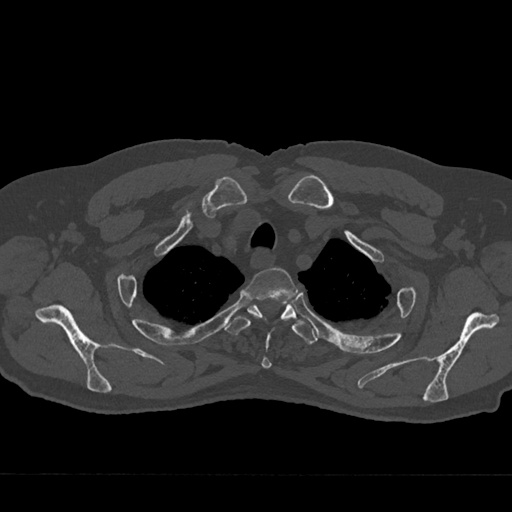
CT including the spine, one axial slice; slice 589 of 797 in the series (ordered by position); reconstruction kernel Br40s/3; 120 kVp; bone window (W 1800 / L 400 HU); 0.5 mm slice thickness; 512 × 512 image matrix, field of view 377 × 377 mm. Male patient, age 75 years. Case-level facts recorded for this patient, not image findings: primary cancer: renal; vertebrae with lytic lesions (as recorded): T4.
Annotated regions visible in this slice (semi-automatic segmentation, software-assisted and operator-edited):
- T2 vertebra: bounding box (x1, y1, x2, y2) in pixels: (246, 267, 297, 369)
- T3 vertebra: (226, 298, 318, 345)